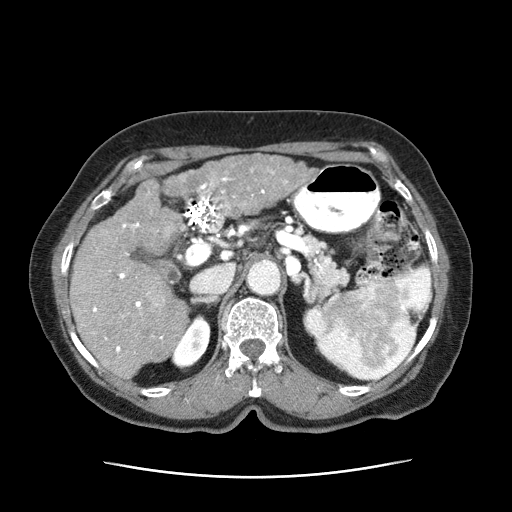
Contrast-enhanced abdominal CT (liver protocol), one axial slice; position 33 of 63 along the scan axis; reconstruction kernel STANDARD; 120 kVp; intravenous contrast given; soft-tissue window (W 400 / L 40 HU); 2.5 mm slice thickness; 512 × 512 image matrix, field of view 360 × 360 mm. Patient: female, 79 years. From the clinical record (not read from this slice): diagnosis: hepatocellular carcinoma (patient treated with transarterial chemoembolisation; whether this scan precedes or follows treatment is not stated here); TNM stage (as recorded): Stage-II.
Structures marked on this image (semi-automatically segmented with operator editing):
- abdominal aorta: bounding box (x1, y1, x2, y2) in pixels: (247, 259, 282, 295)
- liver parenchyma outside the tumour (the mass and vessels are separate outlines, so this box may not span the whole liver): (69, 179, 188, 380)
- mass: (163, 153, 315, 216)
- liver vessels: (93, 177, 265, 355)